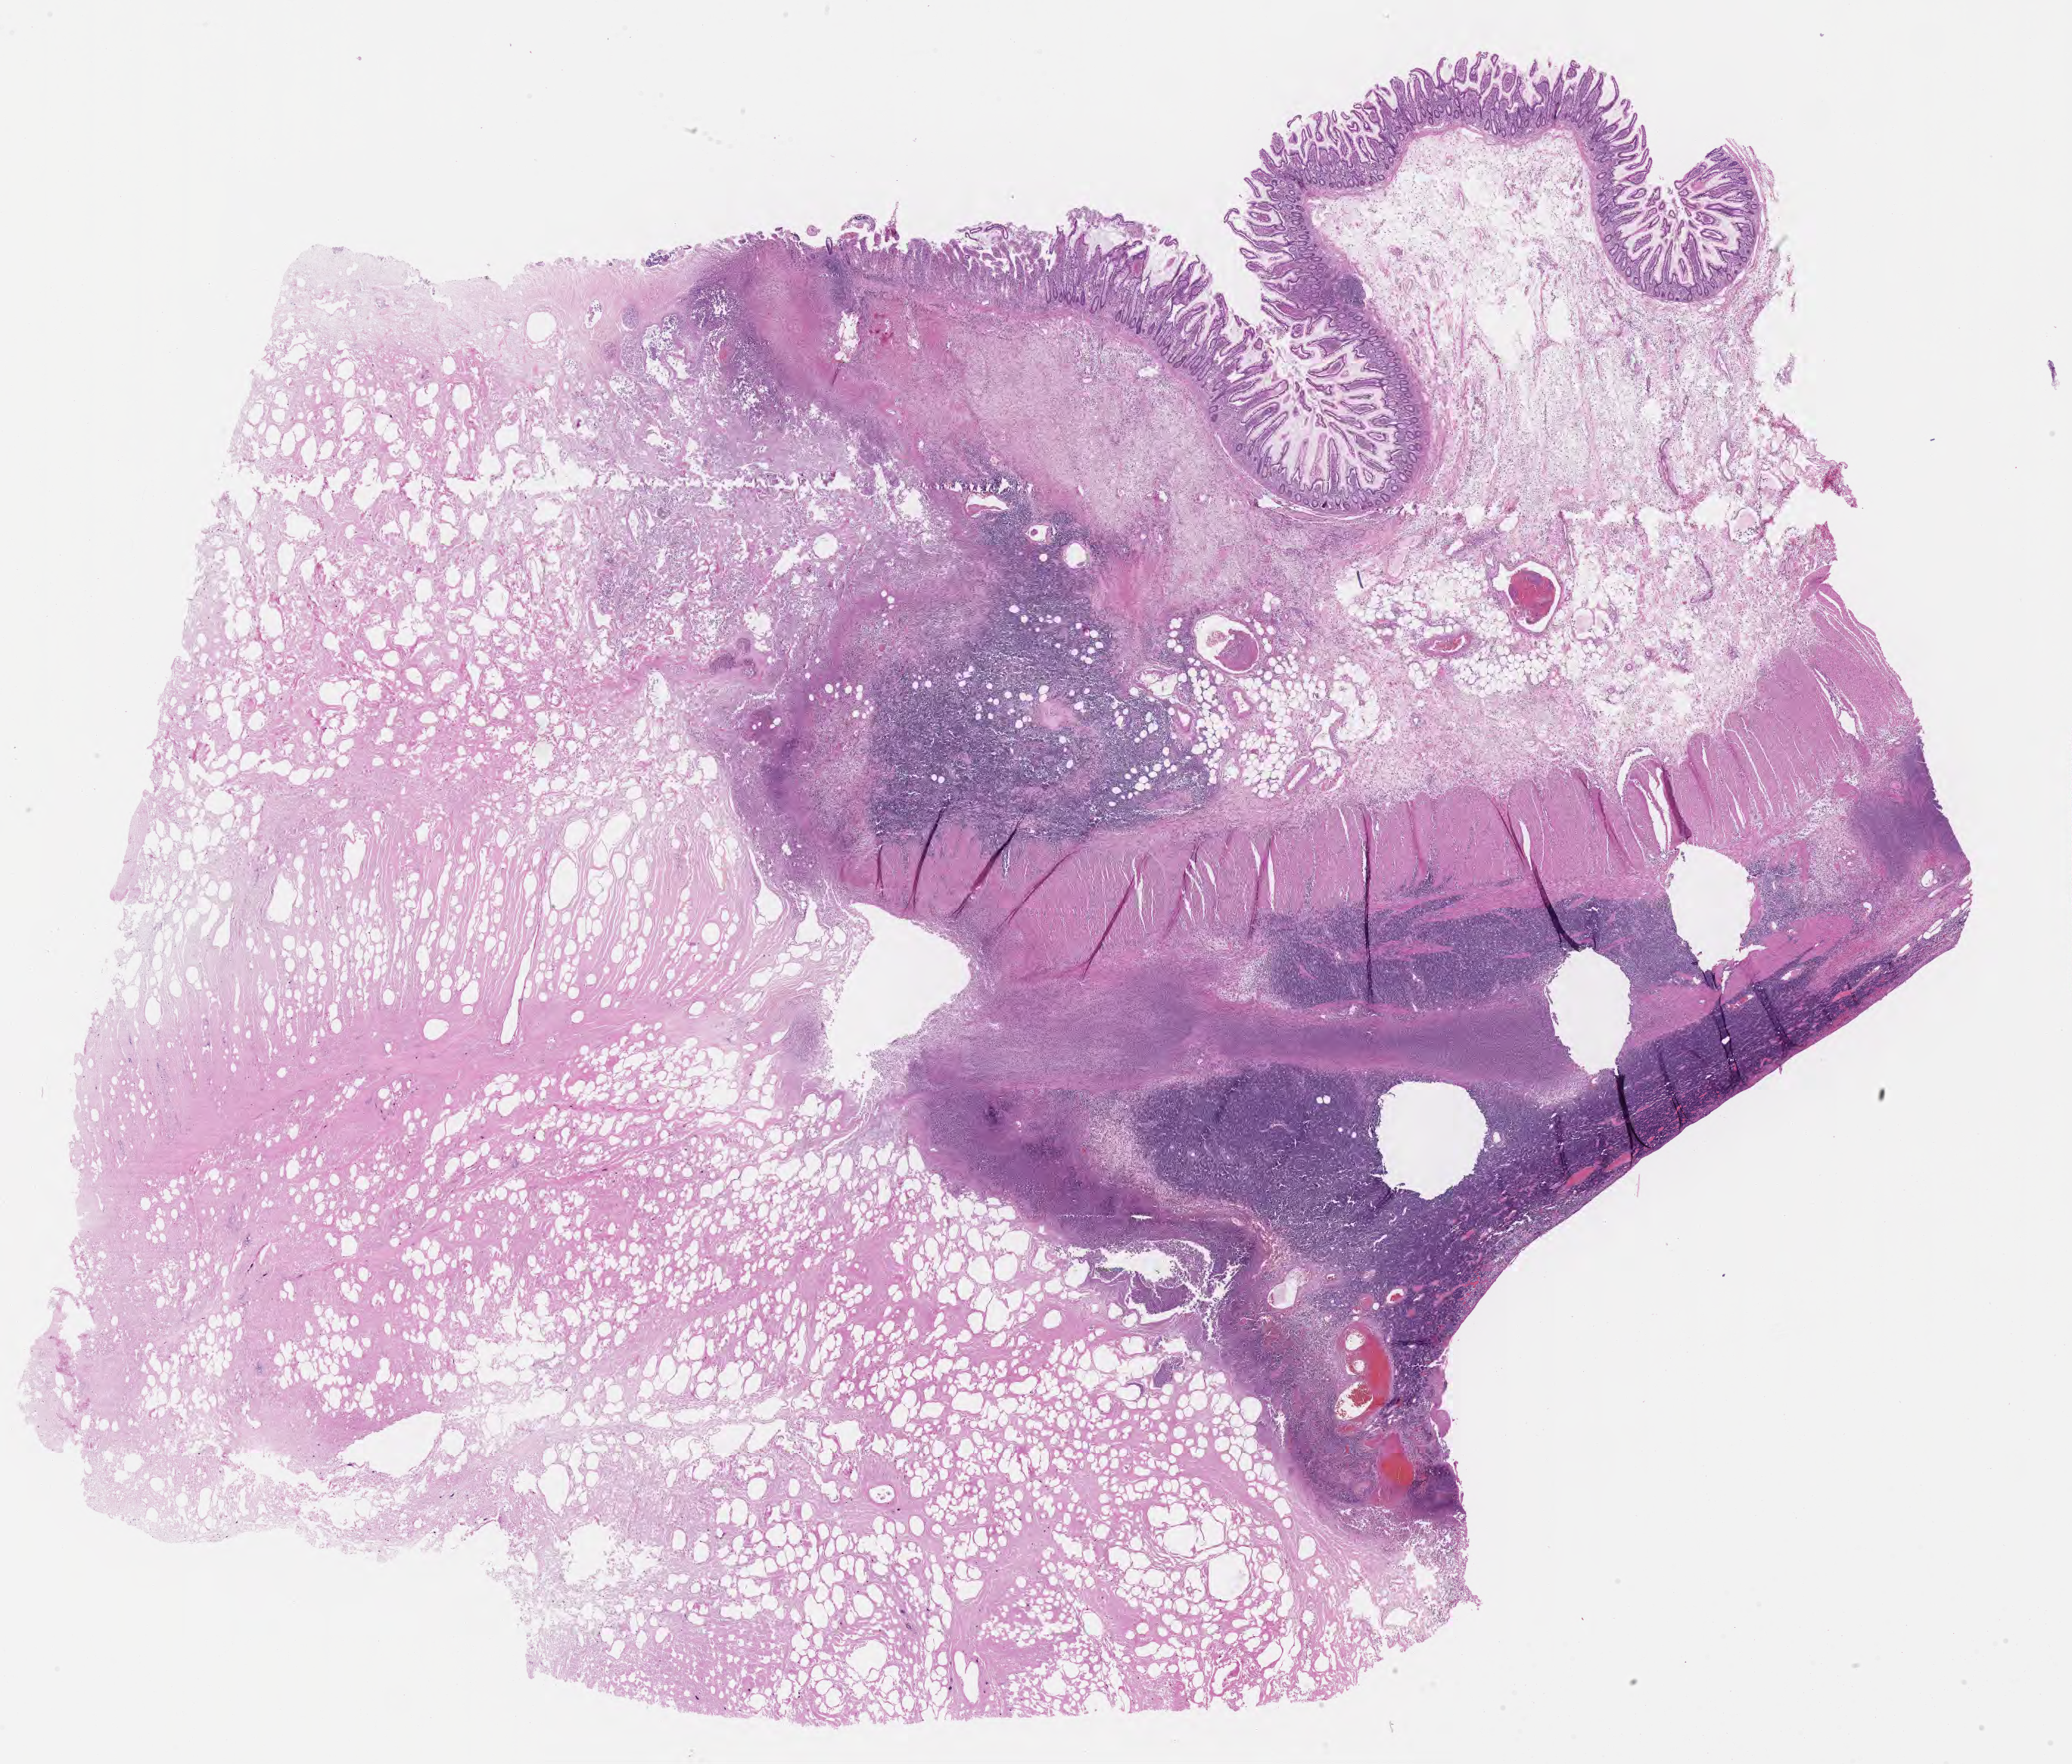
Whole-slide image, haematoxylin and eosin stain — shown as a low-resolution overview of the whole scanned area (about 22.1 x 18.8 mm); tumor tissue; anatomic site: colon. Patient: male, aged 62.
Diagnosis: Burkitt lymphoma, NOS.